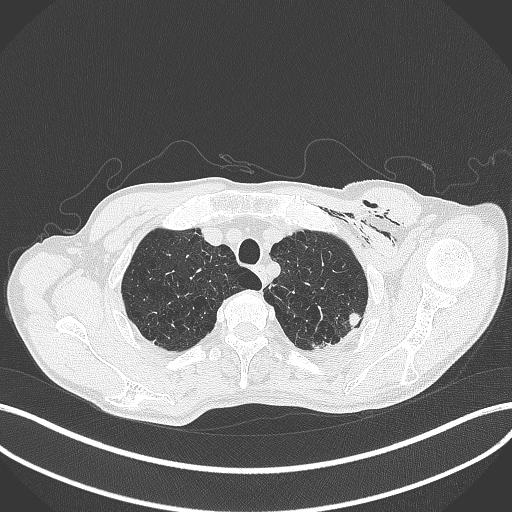
Chest CT, one axial slice. Position 359 of 457 along the scan axis. 120 kVp. Lung window (W 1500 / L -600 HU). 1 mm slice thickness. 512 × 512 image matrix, field of view 400 × 400 mm. Patient: male, 58 years. From the clinical record (not read from this slice): clinical TNM (as recorded): T3 N0 M0.
Outlined on this slice (rectangle marked by the reading radiologist):
- lung tumour (recorded histology: adenocarcinoma): bounding box [x1, y1, x2, y2] px = [348, 311, 364, 329]